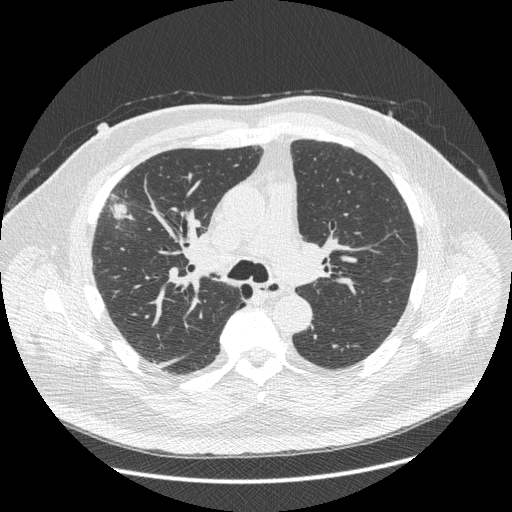
Low-dose screening chest CT, one axial slice; position 271 of 426 along the scan axis; reconstruction kernel STANDARD; lung window (W 1500 / L -600 HU); 512 × 512 image matrix, field of view 400 × 400 mm.
Annotated regions visible in this slice (expert manual segmentation):
- lesion 1 (tumor, upper lobe of right lung): bounding box [x1, y1, x2, y2] px = [113, 204, 127, 215]